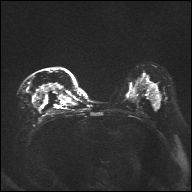
Breast MRI, one axial slice; position 21 of 32 along the scan axis; diffusion-weighted series; image 2 of 4 stored at this slice position (different b-values; order by instance number); 1.5 T; 4 mm slice thickness; 192 × 192 image matrix, field of view 360 × 360 mm. Female patient.
Annotated regions visible in this slice (manually delineated by an expert):
- tumour on diffusion-weighted imaging: bounding box [x1, y1, x2, y2] px = [40, 85, 59, 97]